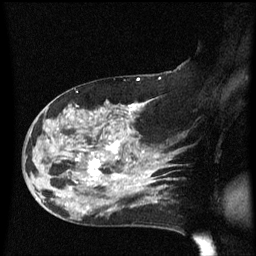
Breast MRI (dynamic contrast-enhanced), one sagittal slice. Position 36 of 60 along the scan axis. Dynamic contrast-enhanced series, image 2 of 3 at this slice position (ordered by acquisition). 1.5 T. TE 4.2 ms, TR 8.4 ms. 256 × 256 image matrix, field of view 200 × 200 mm. Female patient, age 47 years.
Annotated regions visible in this slice (semi-automatic segmentation, software-assisted and operator-edited):
- analysis volume of interest (the breast-tissue region the enhancement analysis was run in; not a lesion): bounding box <24,97,149,206> (left, top, right, bottom; pixels)
- tumour enhancement mask (voxels above the 70 % enhancement threshold inside the analysis volume of interest): <56,102,149,198>